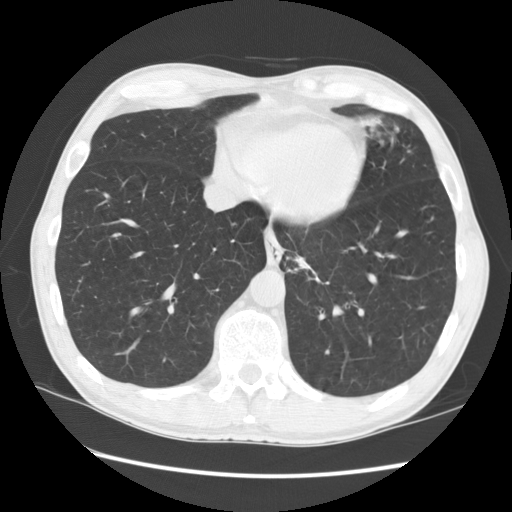
Low-dose screening chest CT, axial slice, baseline annual screen, lung window (W 1500 / L -600 HU), 2.5 mm slice thickness, 512 × 512 image matrix, field of view 360 × 360 mm. Male participant, aged 57 years at enrolment. Current smoker at enrolment.
Expert reader's lesion annotation, bounding box <270,237,334,298> (left, top, right, bottom; pixels). The screening reader recorded 2 non-calcified nodules or masses ≥4 mm on this exam (left lower lobe, lingula); which of them this box marks is not recorded. Participant outcome: lung cancer diagnosed 95 days after this screen — squamous cell carcinoma, NOS, left lower lobe, moderately differentiated (G2), stage IB (AJCC 6th edition), 35 mm at pathology.